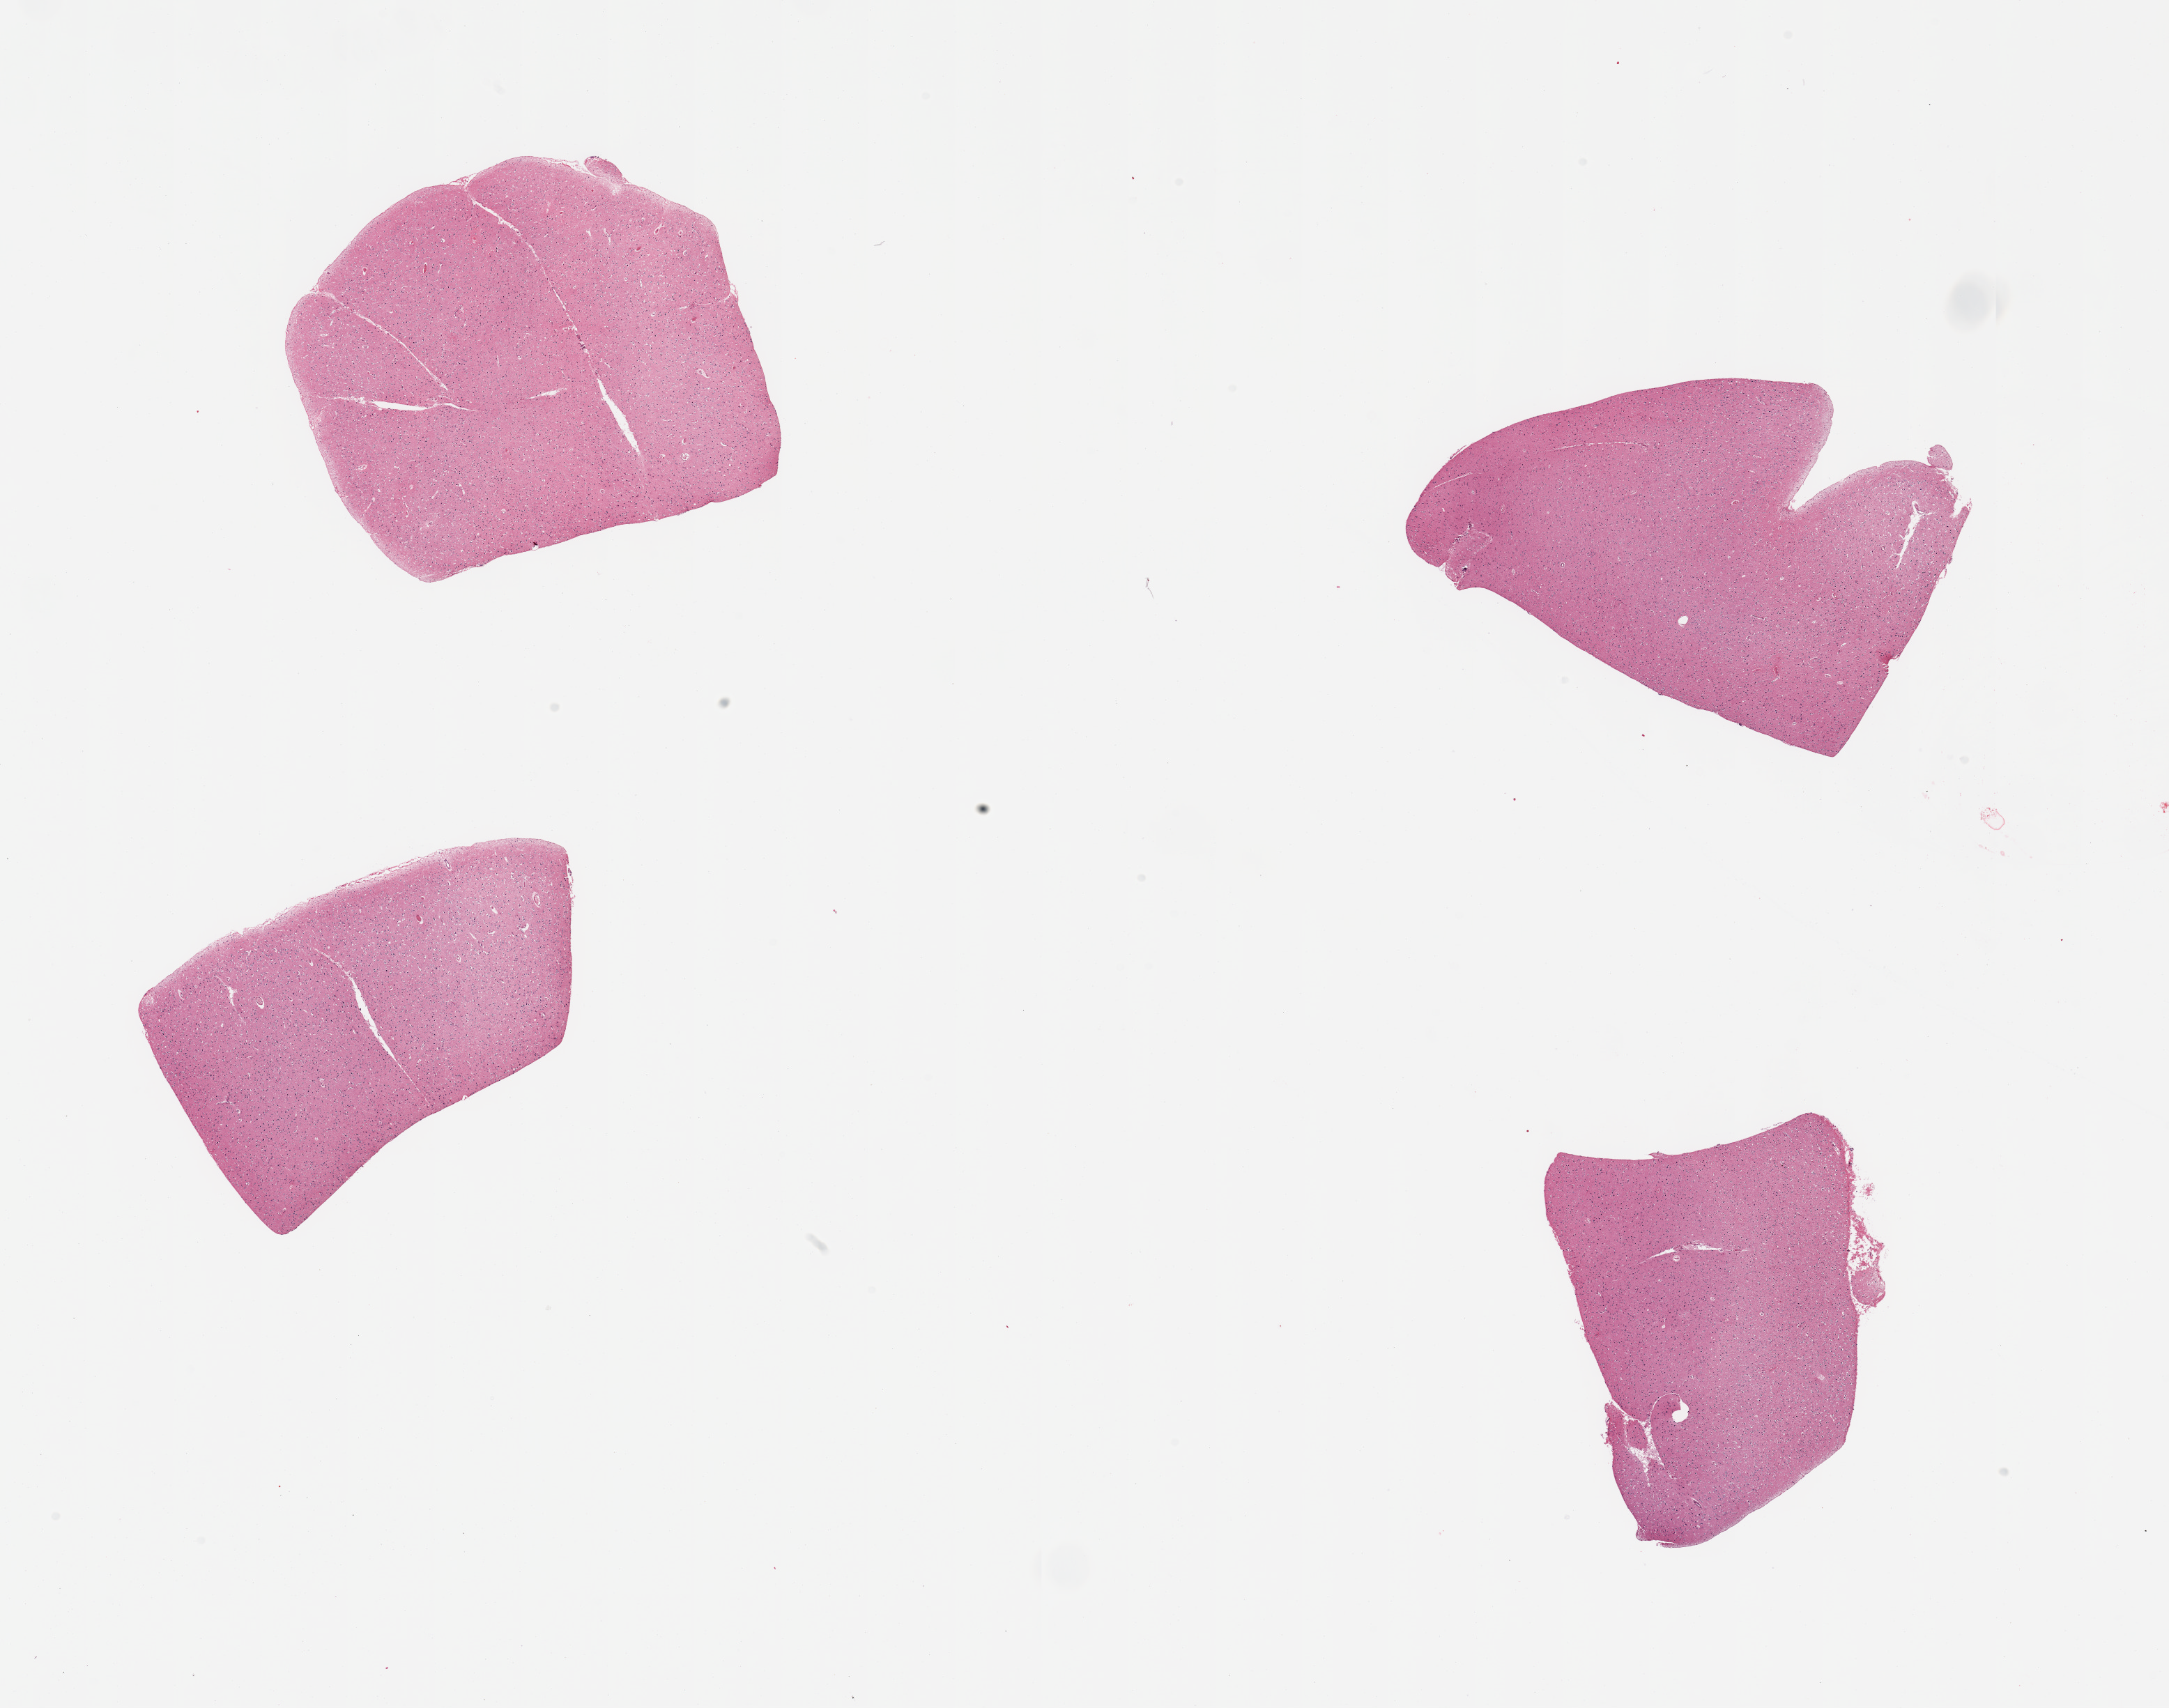
Whole-slide image, H&E stain, brightfield — low-resolution overview of the scanned area, about 24.6 x 19.4 mm; PAXgene-fixed paraffin-embedded (PFPE) section; section of cerebral cortex (target tissue); tissue donor sample. Donor sex: female.
Pathologist's review note for this sample: 4 pieces.